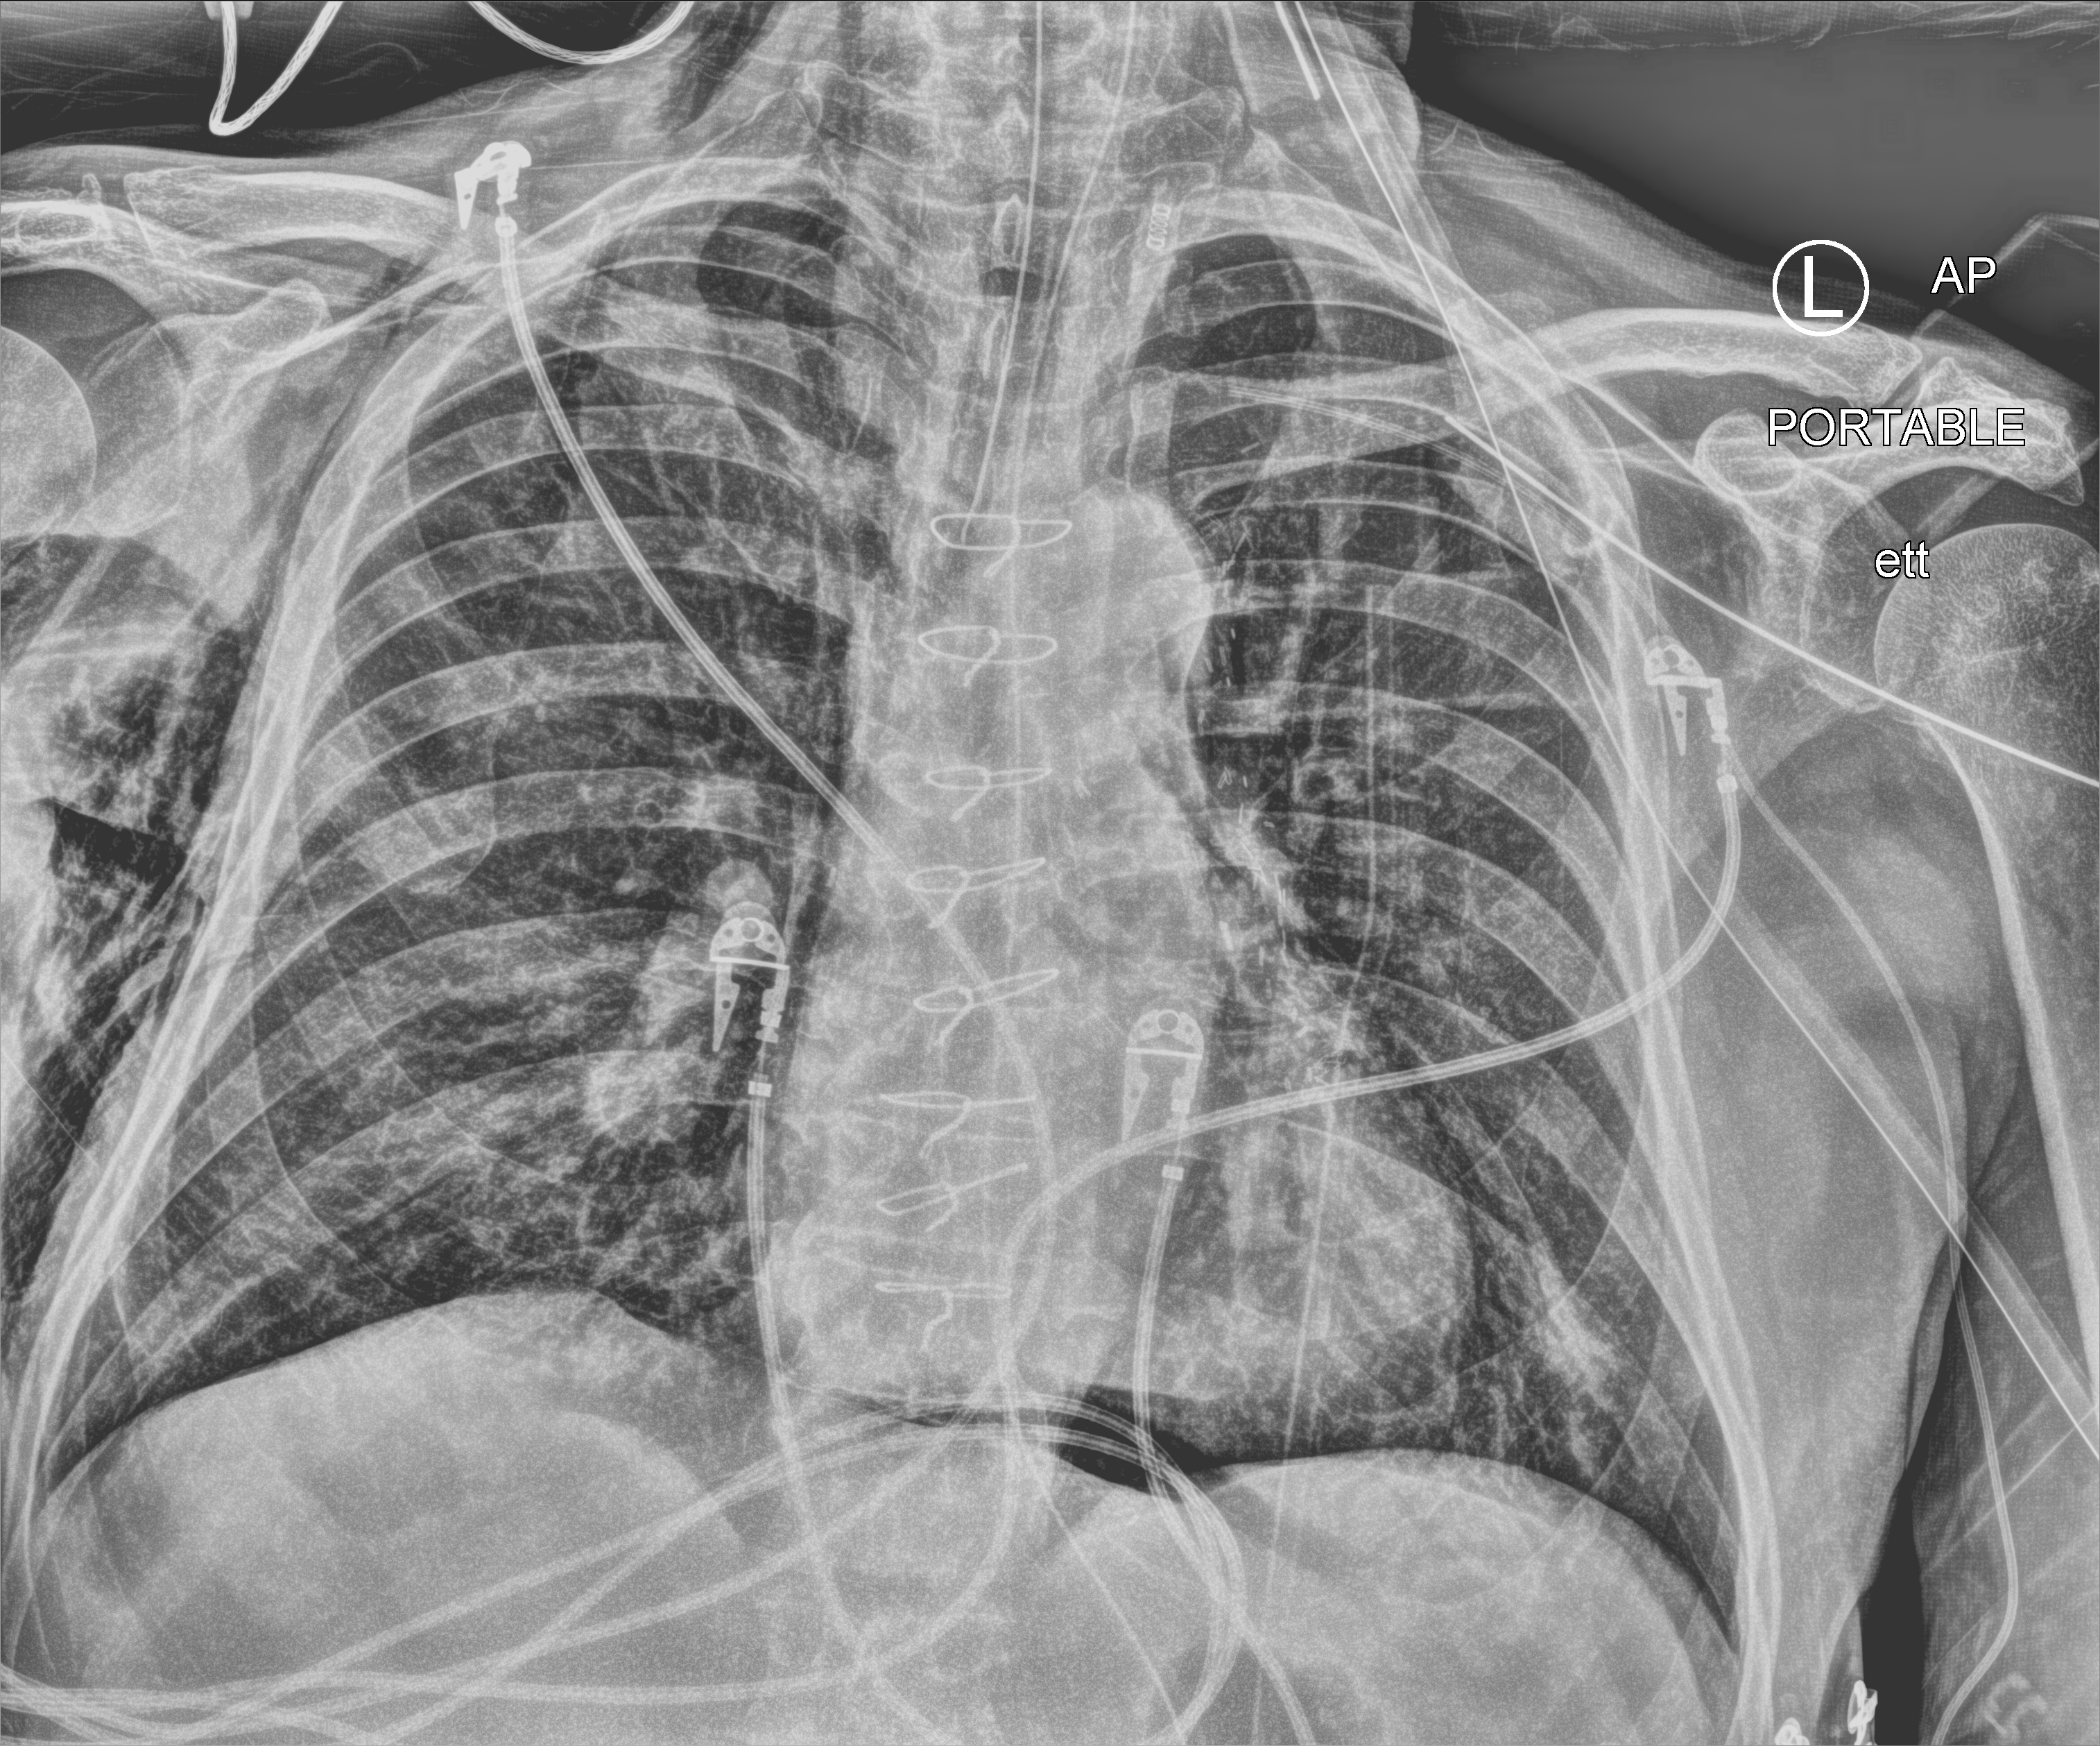
Chest X-ray (portable); anteroposterior (AP) projection. Male patient hospitalised with COVID-19, age 60–74 years.
Hospital-stay facts (about this admission, not read from this image; timing relative to this image not recorded): admitted to intensive care during this hospital stay: yes; chronic kidney disease (admission record): no; mechanically ventilated during this hospital stay: yes.